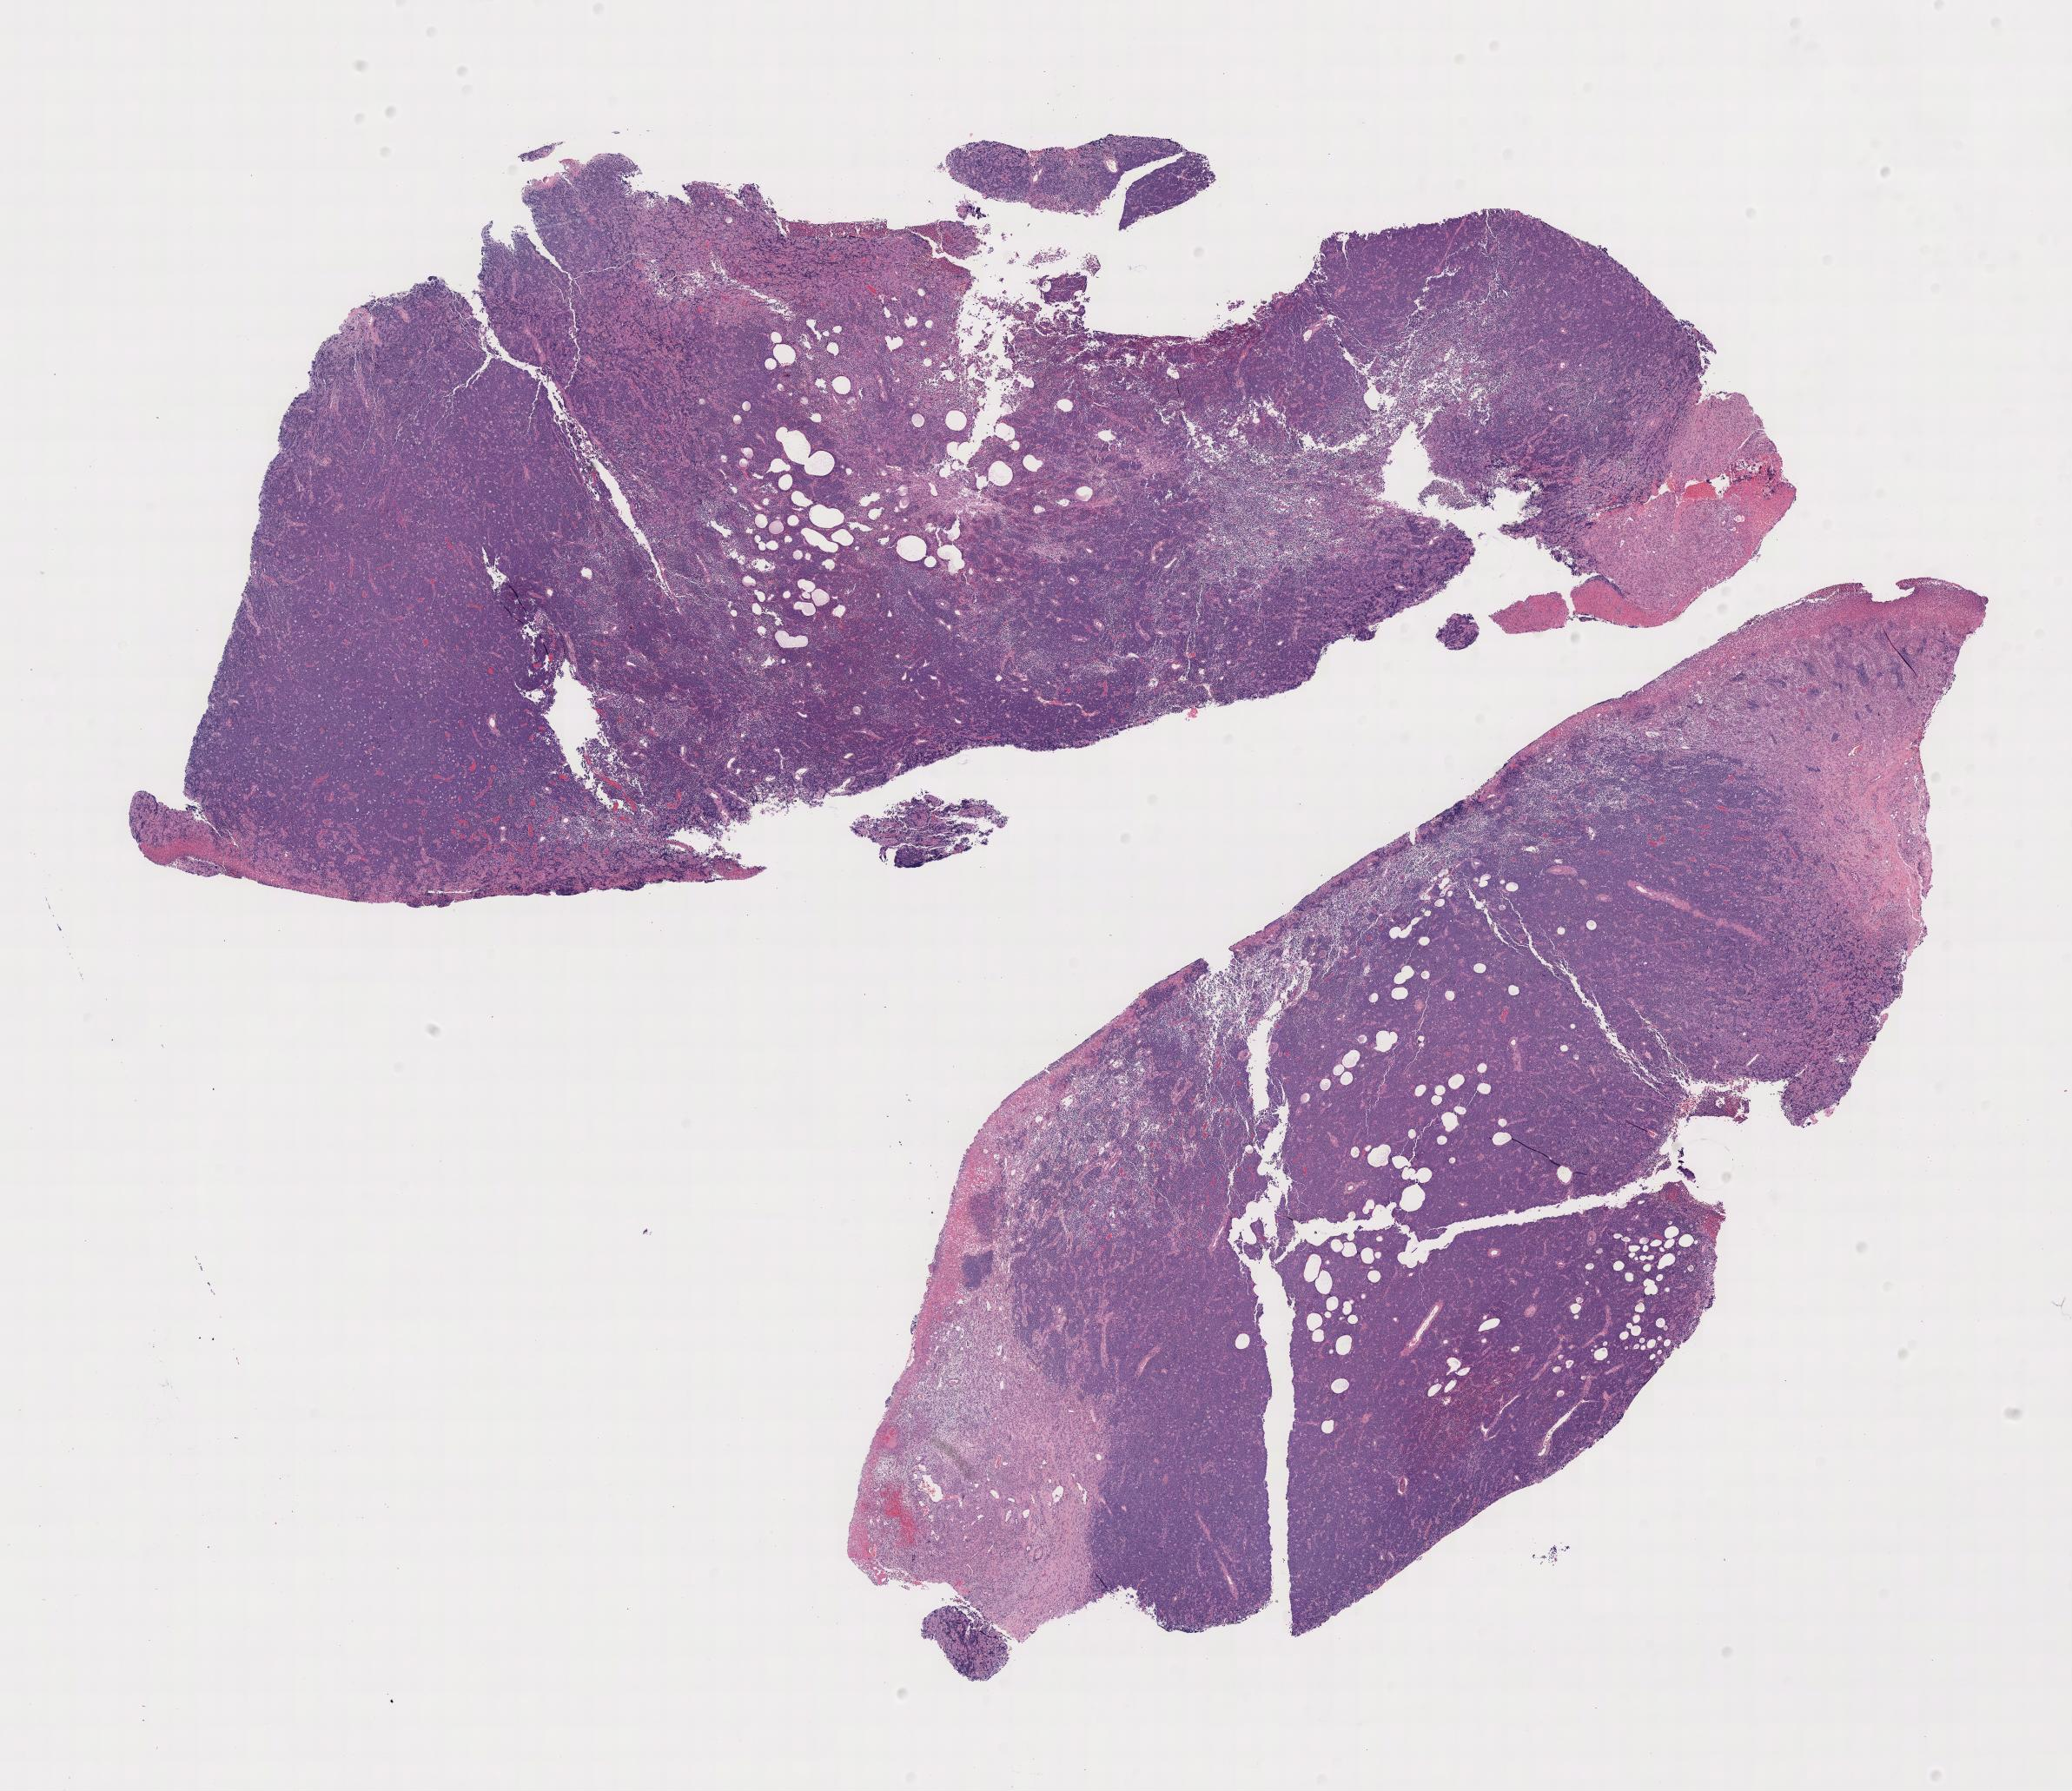
Whole-slide image, hematoxylin and eosin (H&E) stain — low-resolution overview of the scanned area; specimen: tumor tissue; site: cranium. Female, age 6 years at initial diagnosis.
Histologic diagnosis: Burkitt lymphoma, NOS.